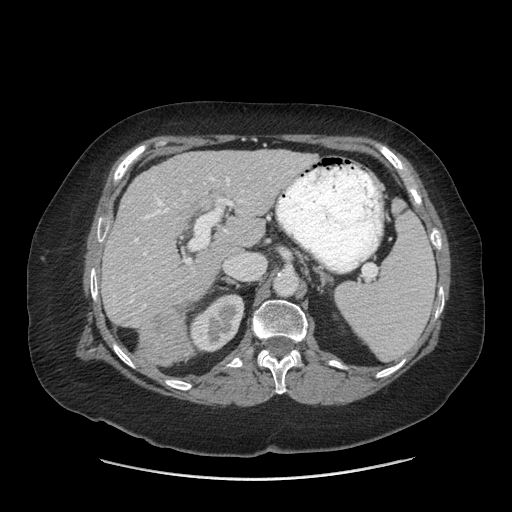
Contrast-enhanced abdominal CT (liver protocol), one axial slice. Slice 39 of 69 in the series (ordered by position). Reconstruction kernel STANDARD. 140 kVp. Soft-tissue window (W 400 / L 40 HU). 2.5 mm slice thickness. 512 × 512 image matrix, field of view 420 × 420 mm. Case-level facts recorded for this patient, not image findings: diagnosis: hepatocellular carcinoma (patient treated with transarterial chemoembolisation; whether this scan precedes or follows treatment is not stated here); TNM stage (as recorded): Stage-IIIB; Child-Pugh class: A.
Annotated regions visible in this slice (semi-automatically segmented with operator editing):
- liver parenchyma outside the tumour (the mass and vessels are separate outlines, so this box may not span the whole liver): bounding box <102,150,316,328> (left, top, right, bottom; pixels)
- mass: <141,312,190,364>
- liver vessels: <130,177,243,307>